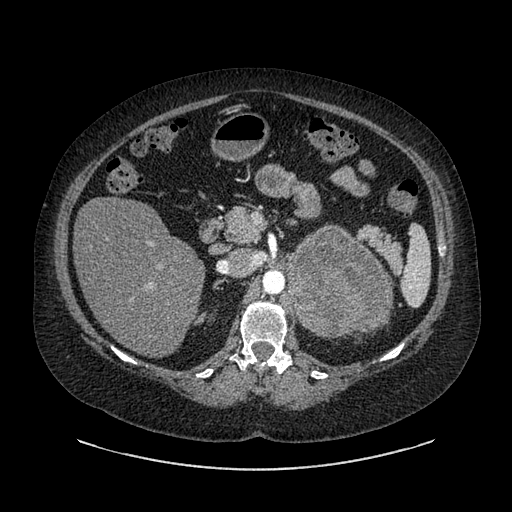
Contrast-enhanced abdominal CT, one axial slice; position 557 of 769 along the scan axis; reconstruction kernel SOFT; intravenous contrast given; soft-tissue window (W 400 / L 40 HU); 0.62 mm slice thickness; 512 × 512 image matrix, field of view 460 × 460 mm. Patient: female, 61 years. Case-level facts recorded for this patient, not image findings: diagnosis: adrenocortical carcinoma; tumour side: left adrenal; tumour size at pathology: 13 cm; Ki-67 index: 79 %; stage (as recorded): 2.
Outlined on this slice (semi-automatically segmented with operator editing):
- mass: bounding box [x1, y1, x2, y2] px = [286, 229, 391, 339]